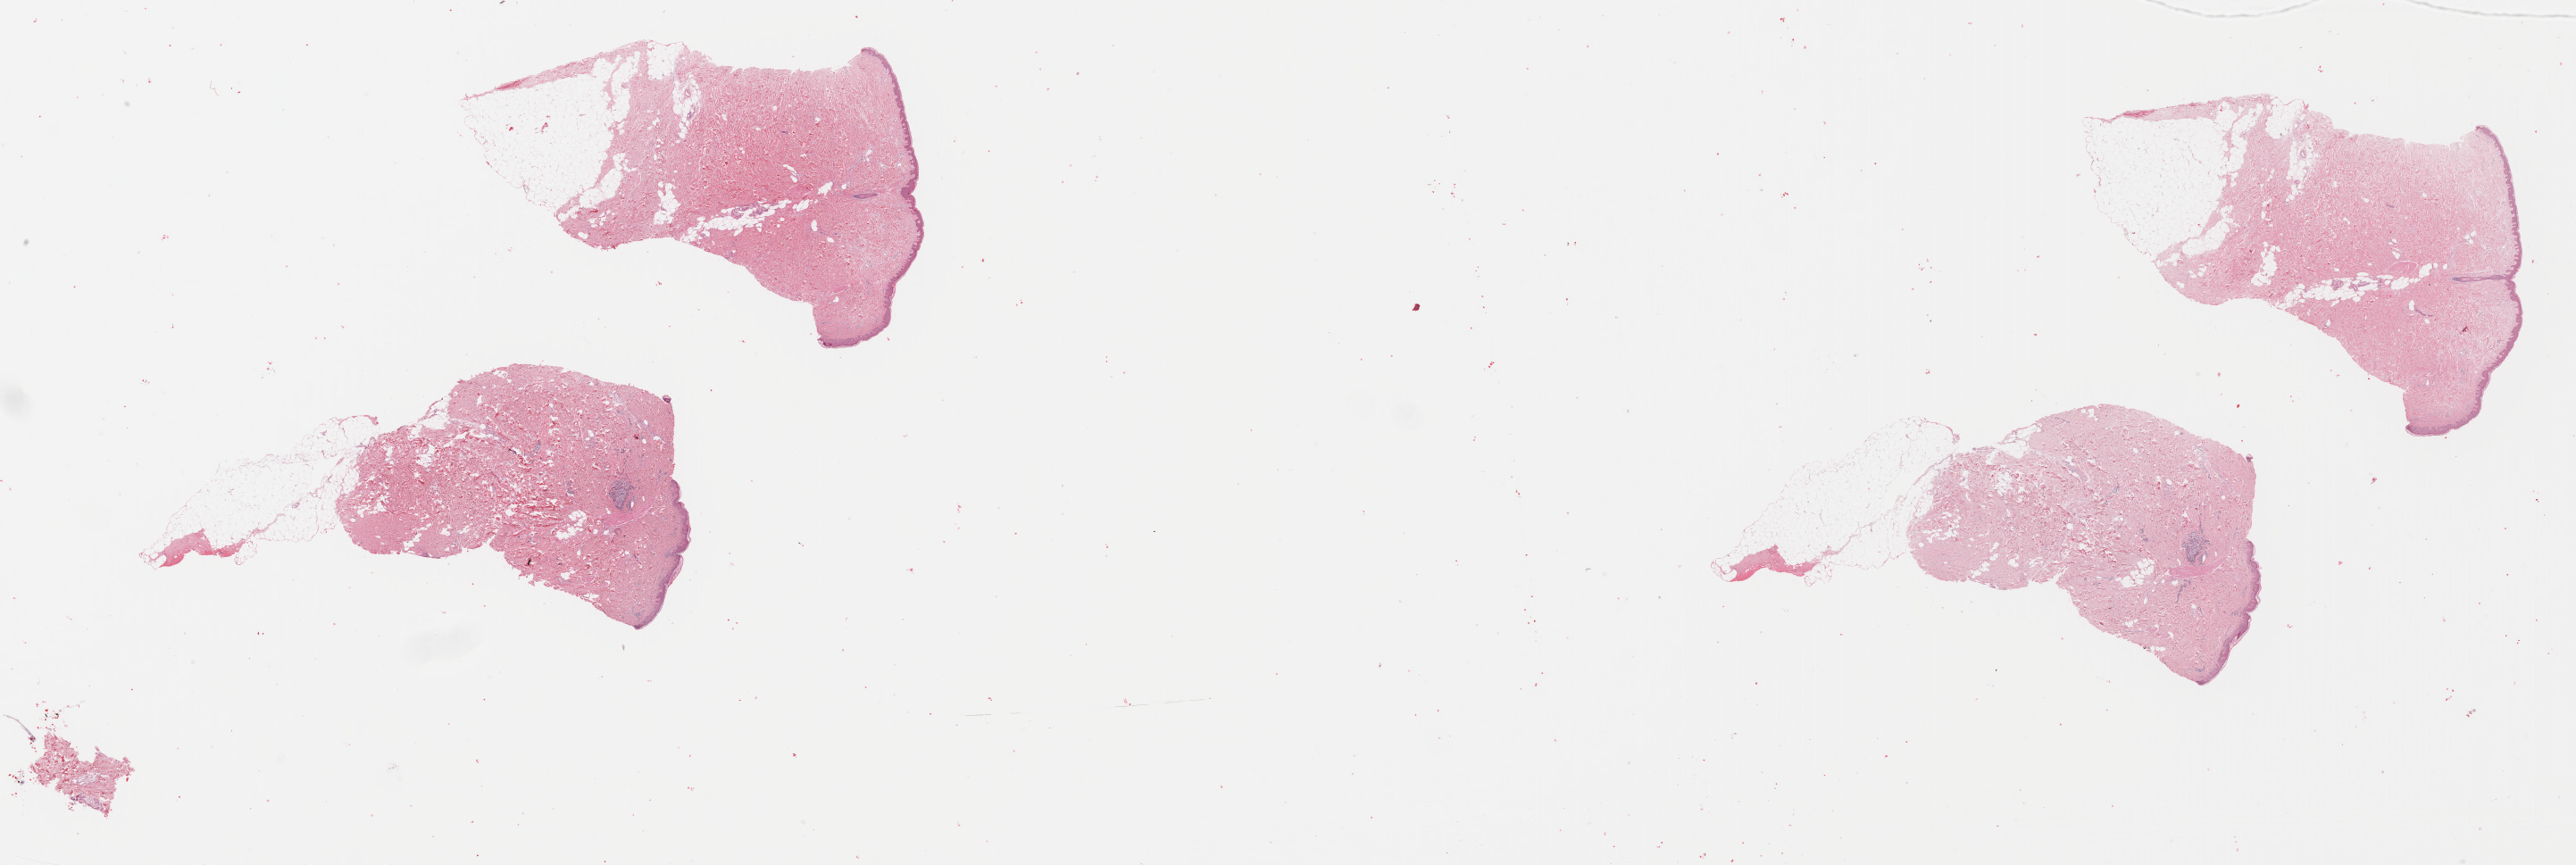
Digitized Hematoxylin and eosin (H&E) stained tissue section (whole slide), low-resolution overview of the scanned area, about 45.4 x 15.2 mm, FFPE section, metastatic tumour sample, sampled site: skin. Female, age 70 years at initial diagnosis.
This section: metastatic tumour tissue. Patient diagnosis: Malignant melanoma, NOS.